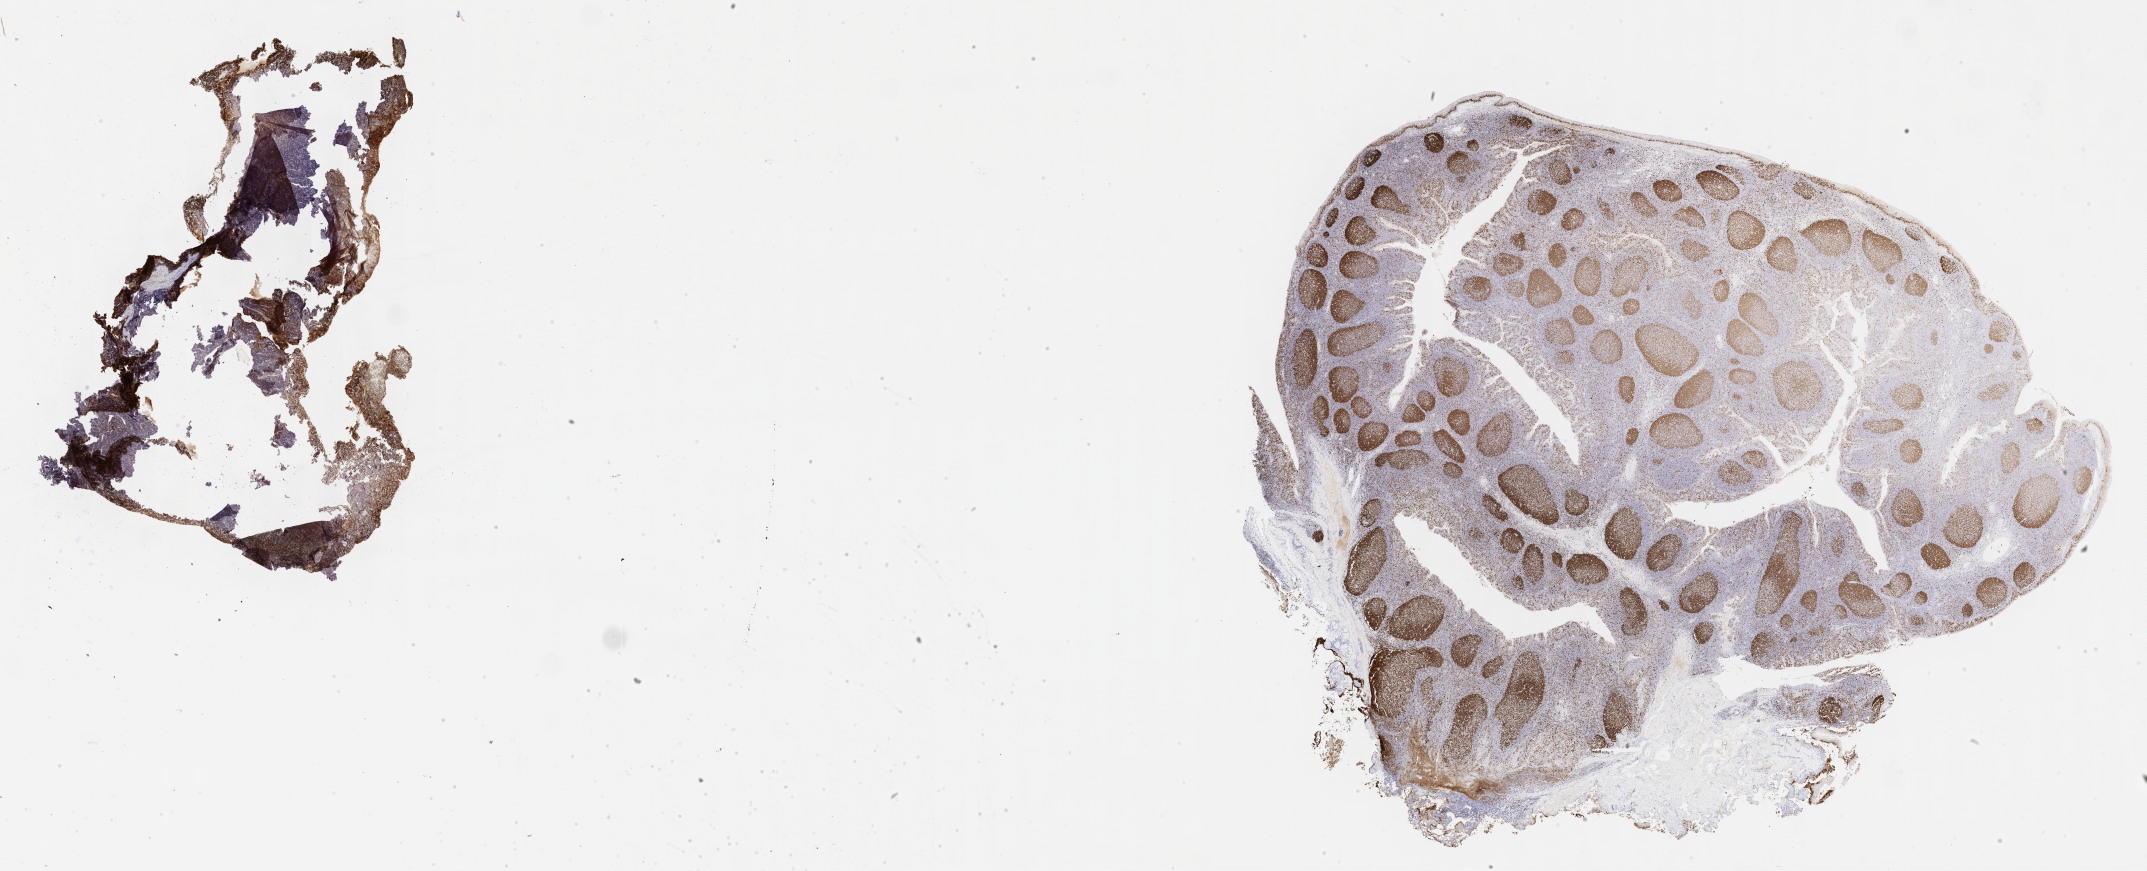
IHC for Ki-67, whole-slide image, whole scanned area (about 34.7 x 14.1 mm) shown as a low-resolution overview; tumor tissue; anatomic site: cranium. Female patient, 10 years old.
- histologic diagnosis: Burkitt lymphoma, NOS